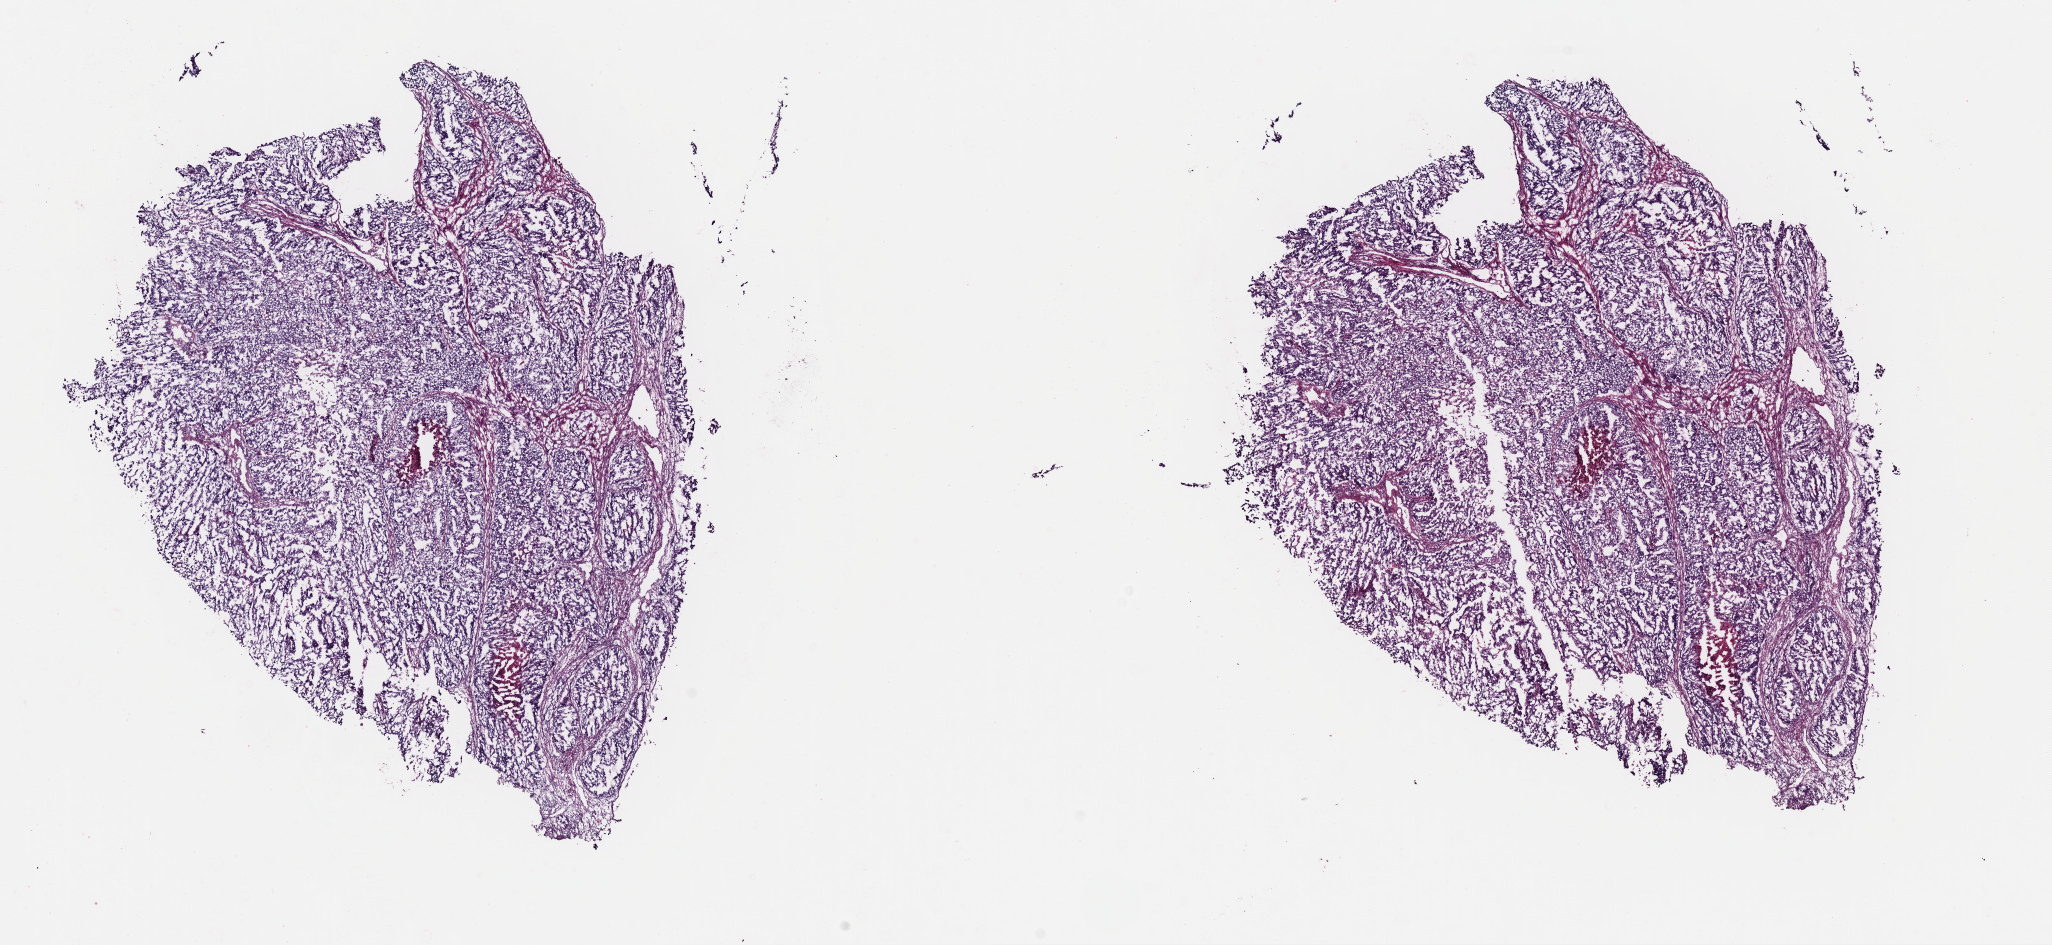
H&E whole-slide image, shown as a low-resolution overview of the whole scanned area (about 16.2 x 7.5 mm, slide scanned at 40x); frozen section from the top of the tissue portion; sample: primary tumour, uterus. Female, age 60 years at initial diagnosis. Histologic grade: G3 (poorly differentiated). Slide review estimates, as recorded: tumour cells 90%, tumour nuclei 94%, normal cells 3%, stromal cells 3%, necrosis 4%. Infiltration values recorded for this section: lymphocyte infiltration 1%, monocyte infiltration 0%, neutrophil infiltration 1%.
* FIGO stage: IIIC
* pathologic diagnosis: Serous cystadenocarcinoma, NOS (endometrium)